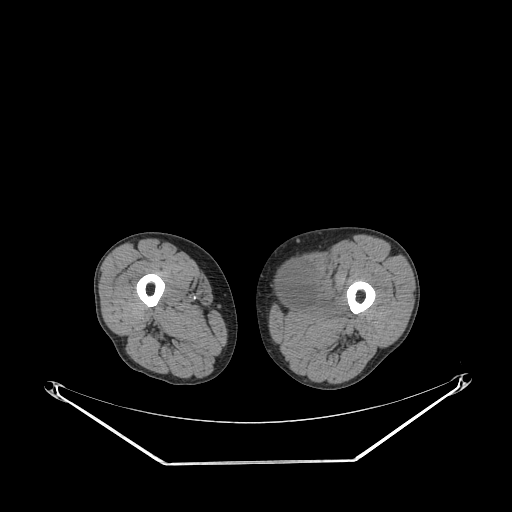
CT of an extremity soft-tissue mass (from a PET/CT study), one axial slice; slice 228 of 267 in the series (ordered by position); reconstruction kernel STANDARD; 140 kVp; soft-tissue window (W 400 / L 40 HU); 3.75 mm slice thickness; 512 × 512 image matrix, field of view 500 × 500 mm. Male patient. Case-level facts recorded for this patient, not image findings: histological type: pleiomorphic liposarcoma; grade: high; site of the primary tumour: left thigh.
Annotated regions visible in this slice (expert contour drawn on MRI and transferred to this co-registered scan by the dataset authors):
- gross tumour volume including surrounding oedema: bounding box (x1, y1, x2, y2) in pixels: (279, 260, 344, 318)
- gross tumour volume (mass): (279, 258, 318, 307)